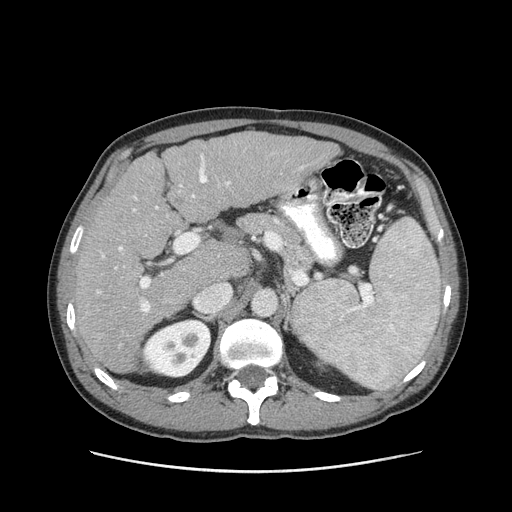
Contrast-enhanced abdominal CT (liver protocol), one axial slice; position 56 of 93 along the scan axis; 120 kVp; soft-tissue window (W 400 / L 40 HU); 2.5 mm slice thickness; 512 × 512 image matrix, field of view 380 × 380 mm. From the clinical record (not read from this slice): diagnosis: hepatocellular carcinoma (patient treated with transarterial chemoembolisation; whether this scan precedes or follows treatment is not stated here); TNM stage (as recorded): Stage-II; Child-Pugh class: A; tumour differentiation: moderately differentiated; tumour nodularity: multinodular.
Outlined on this slice (semi-automatic segmentation, software-assisted and operator-edited):
- liver parenchyma outside the tumour (the mass and vessels are separate outlines, so this box may not span the whole liver): box from (x=74, y=132) to (x=338, y=372) px
- liver vessels: (x=97, y=154)–(x=304, y=313)